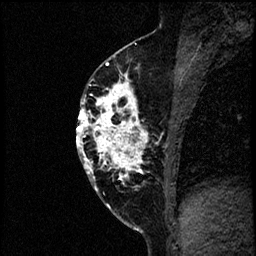
Breast MRI (dynamic contrast-enhanced), one sagittal slice. Position 33 of 60 along the scan axis. Dynamic contrast-enhanced study with each time point stored as its own series, time point 2 of 4 at this slice position (early post-contrast, ordered by acquisition time). 1.5 T. TE 4.2 ms, TR 17.6 ms. 2 mm slice thickness. 256 × 256 image matrix, field of view 200 × 200 mm. Patient: female, 40 years. From the clinical record (not read from this slice): setting: breast cancer imaged before/during neoadjuvant chemotherapy; receptor status: HER2-positive.
Annotated regions visible in this slice (semi-automatically segmented with operator editing):
- analysis volume of interest (the breast-tissue region the enhancement analysis was run in; not a lesion): bounding box (x1, y1, x2, y2) in pixels: (77, 56, 197, 205)
- tumour enhancement mask (voxels above the 100 % enhancement threshold inside the analysis volume of interest): (78, 62, 149, 181)